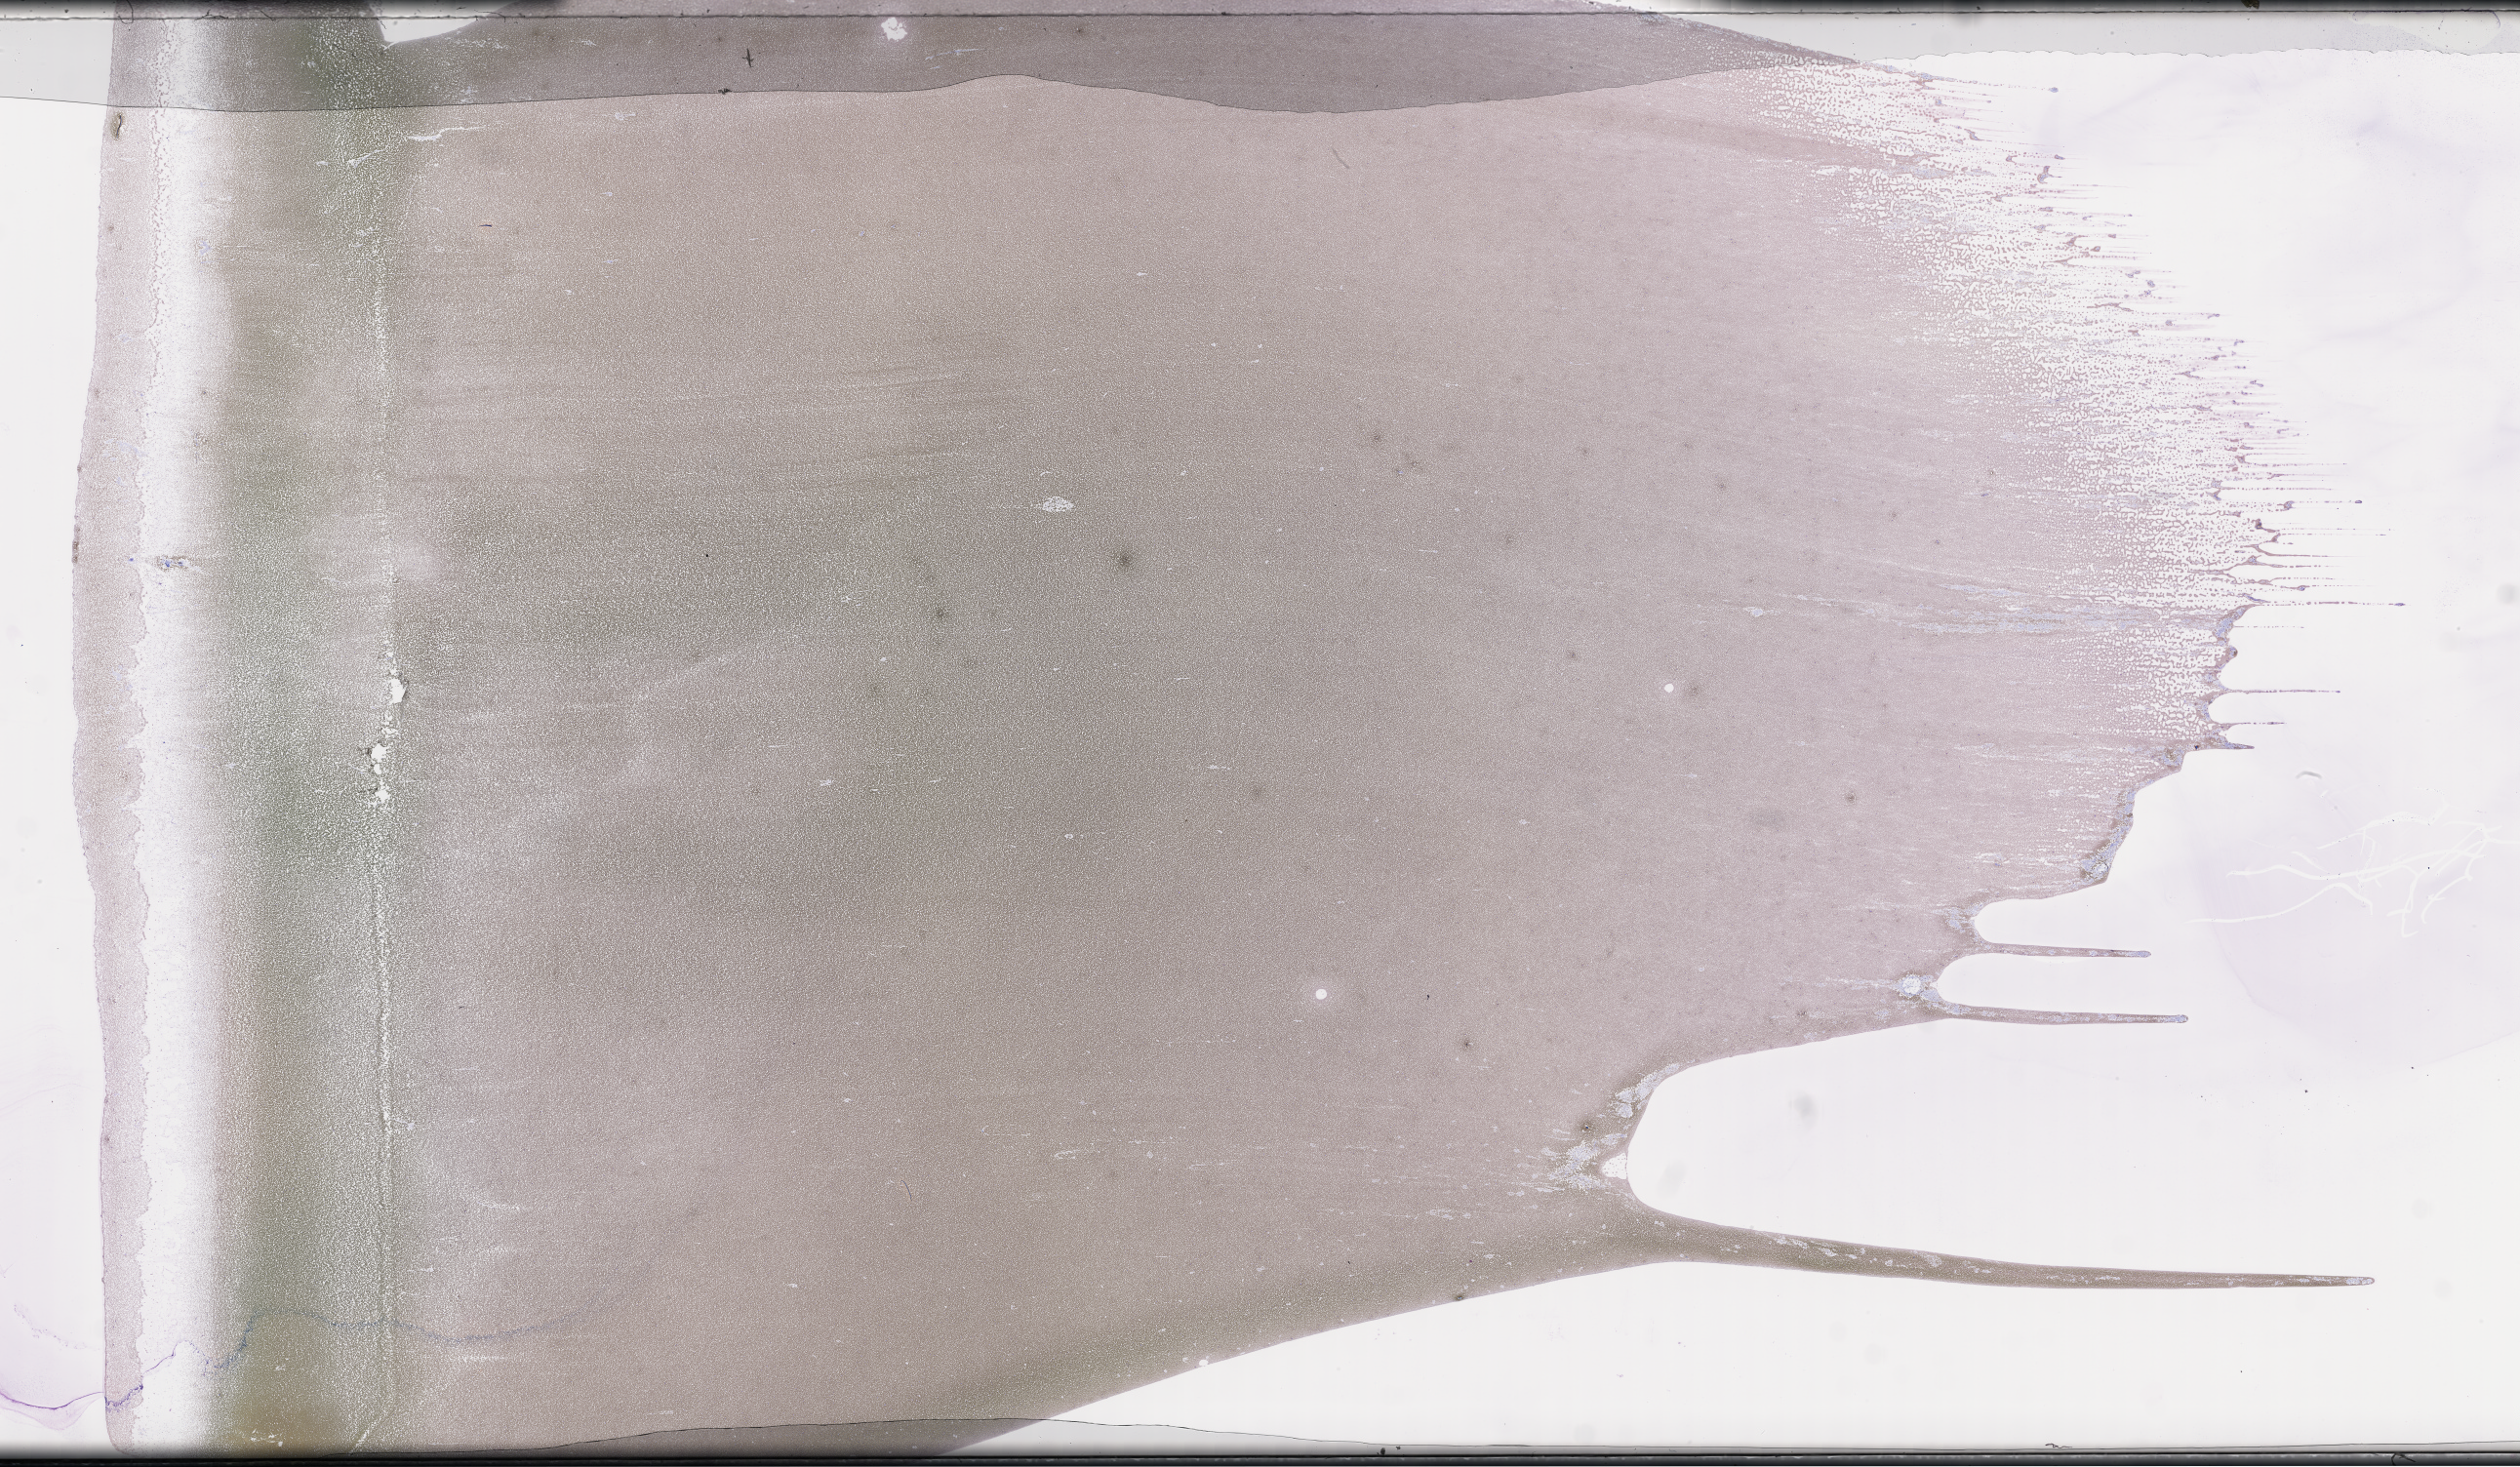
Wright–Giemsa-stained whole blood smear, whole-slide image, shown as a low-resolution overview of the whole scanned area (about 41.7 x 24.3 mm), smear from an EDTA sample, specimen time point: collected on treatment. Female patient.
Patient diagnosis: Plasma Cell Myeloma.